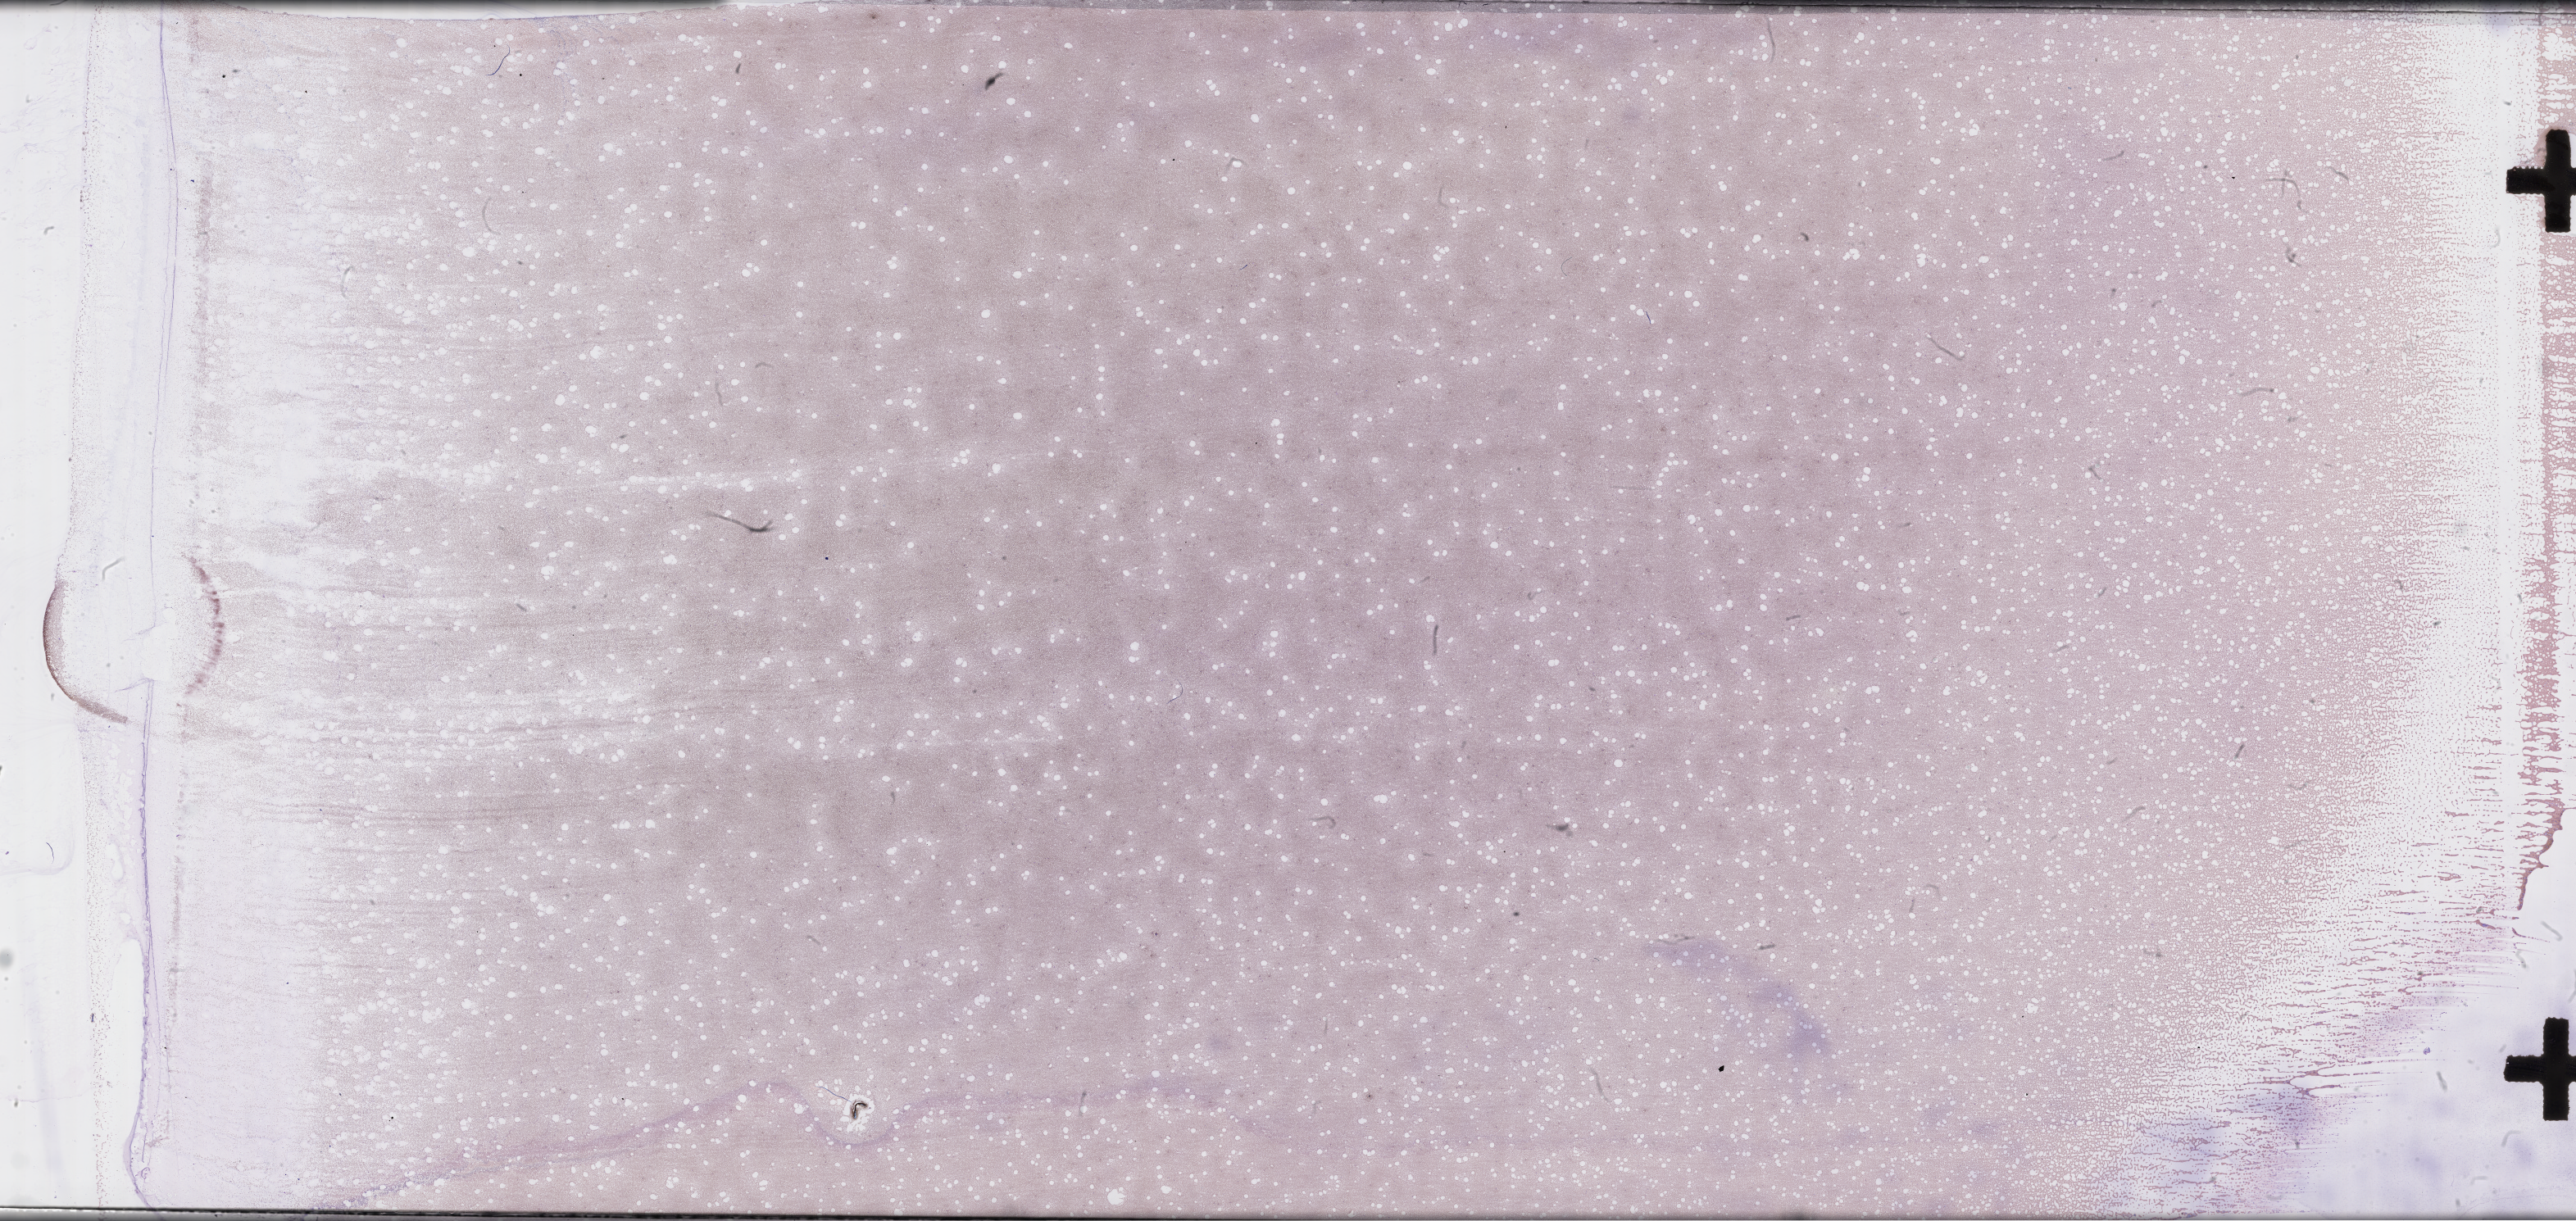
Whole-slide image of a whole blood smear, Wright–Giemsa stain — shown as a low-resolution overview of the whole scanned area (about 50.8 x 24.1 mm). Male patient.
• patient diagnosis: Plasma Cell Myeloma